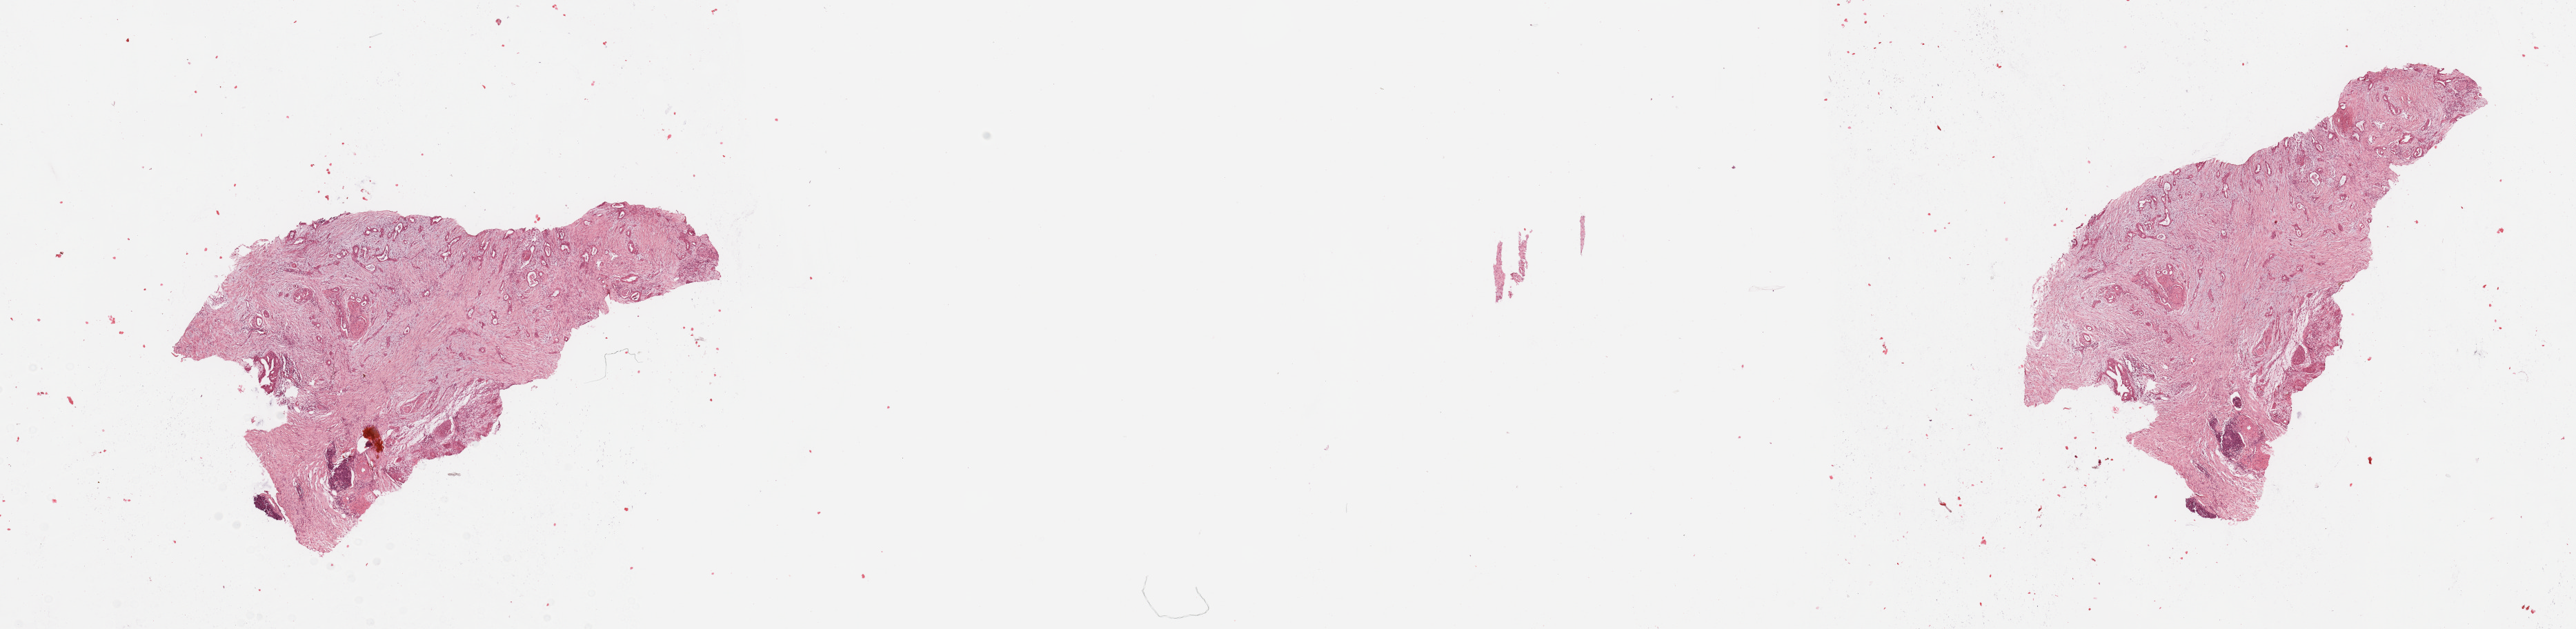
Hematoxylin and eosin (H&E) stained whole-slide image, whole scanned area (about 29.5 x 7.2 mm) shown as a low-resolution overview, tumour tissue sample, sampled site: pancreas. Male, 60 y/o. Histologic grade: G2 (moderately differentiated). Slide review estimates, as recorded: tumour nuclei 25%, necrosis 0%.
AJCC pathologic stage: IIB. Histologic diagnosis: Infiltrating duct carcinoma, NOS. Primary tumour site (as recorded): head.